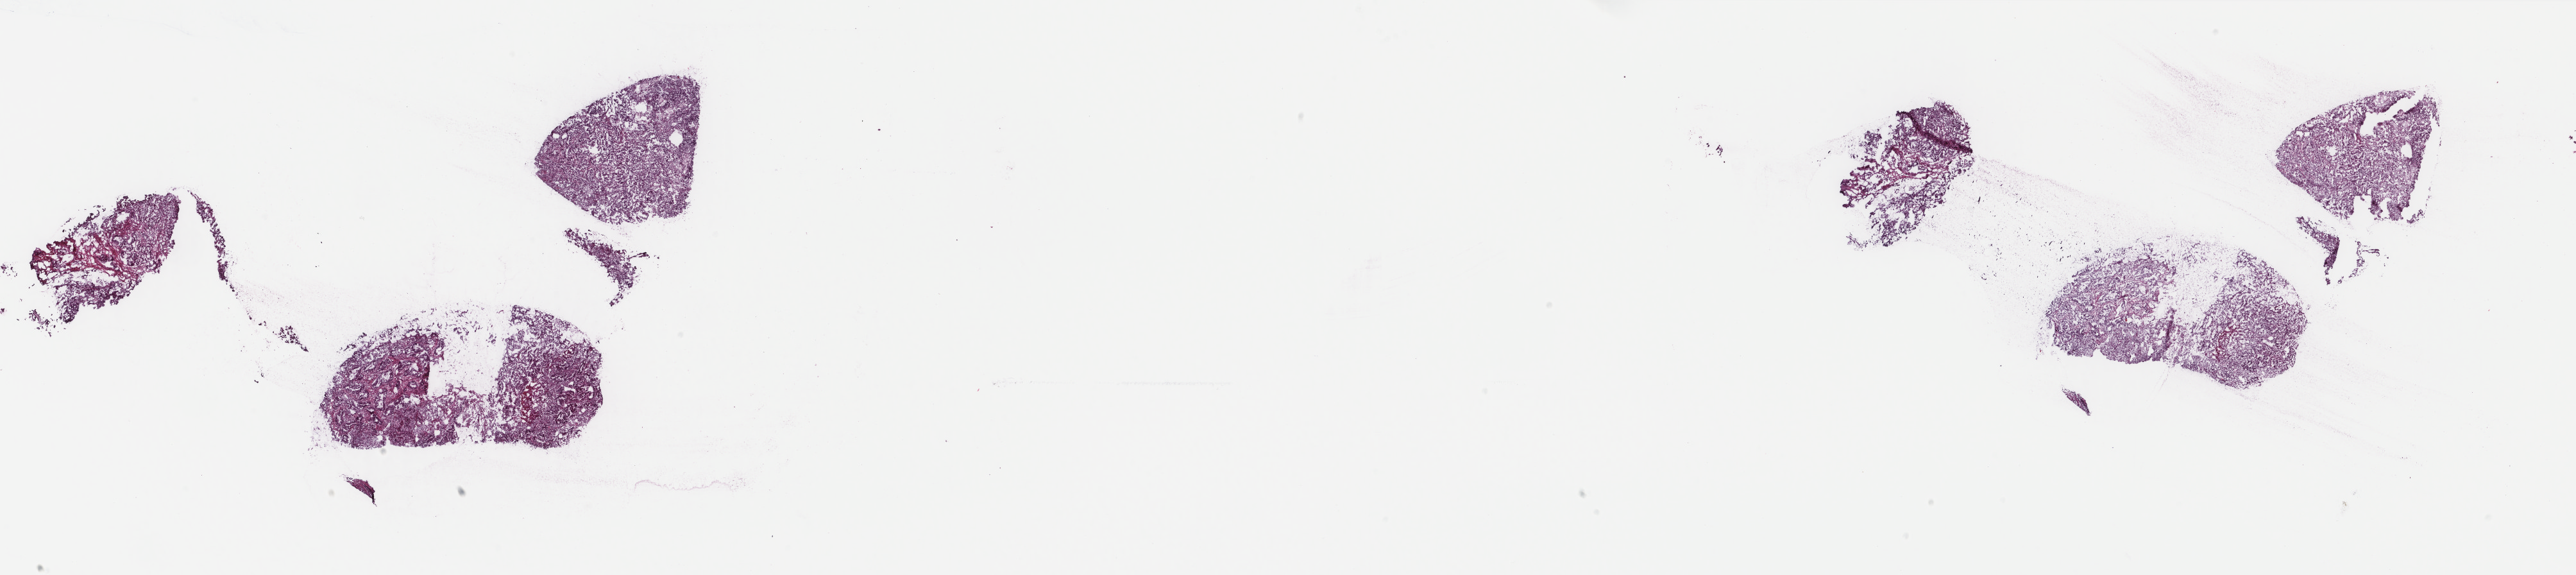
Whole-slide histology image, H&E-stained, shown as a low-resolution overview of the whole scanned area (about 31.9 x 7.1 mm, slide scanned at 40x). Frozen section. Sample: primary tumour, uterus. Female patient; age at initial diagnosis 38 years. Histologic grade: G2 (moderately differentiated). Pathologist review of this section (percent, as recorded): tumour cells 80%, tumour nuclei 80%, normal cells 0%, stromal cells 10%, necrosis 10%. Inflammatory infiltration, as recorded: lymphocyte infiltration 40%, monocyte infiltration 20%, neutrophil infiltration 20%.
FIGO stage: IB. Pathologic diagnosis: Endometrioid adenocarcinoma, NOS (endometrium).